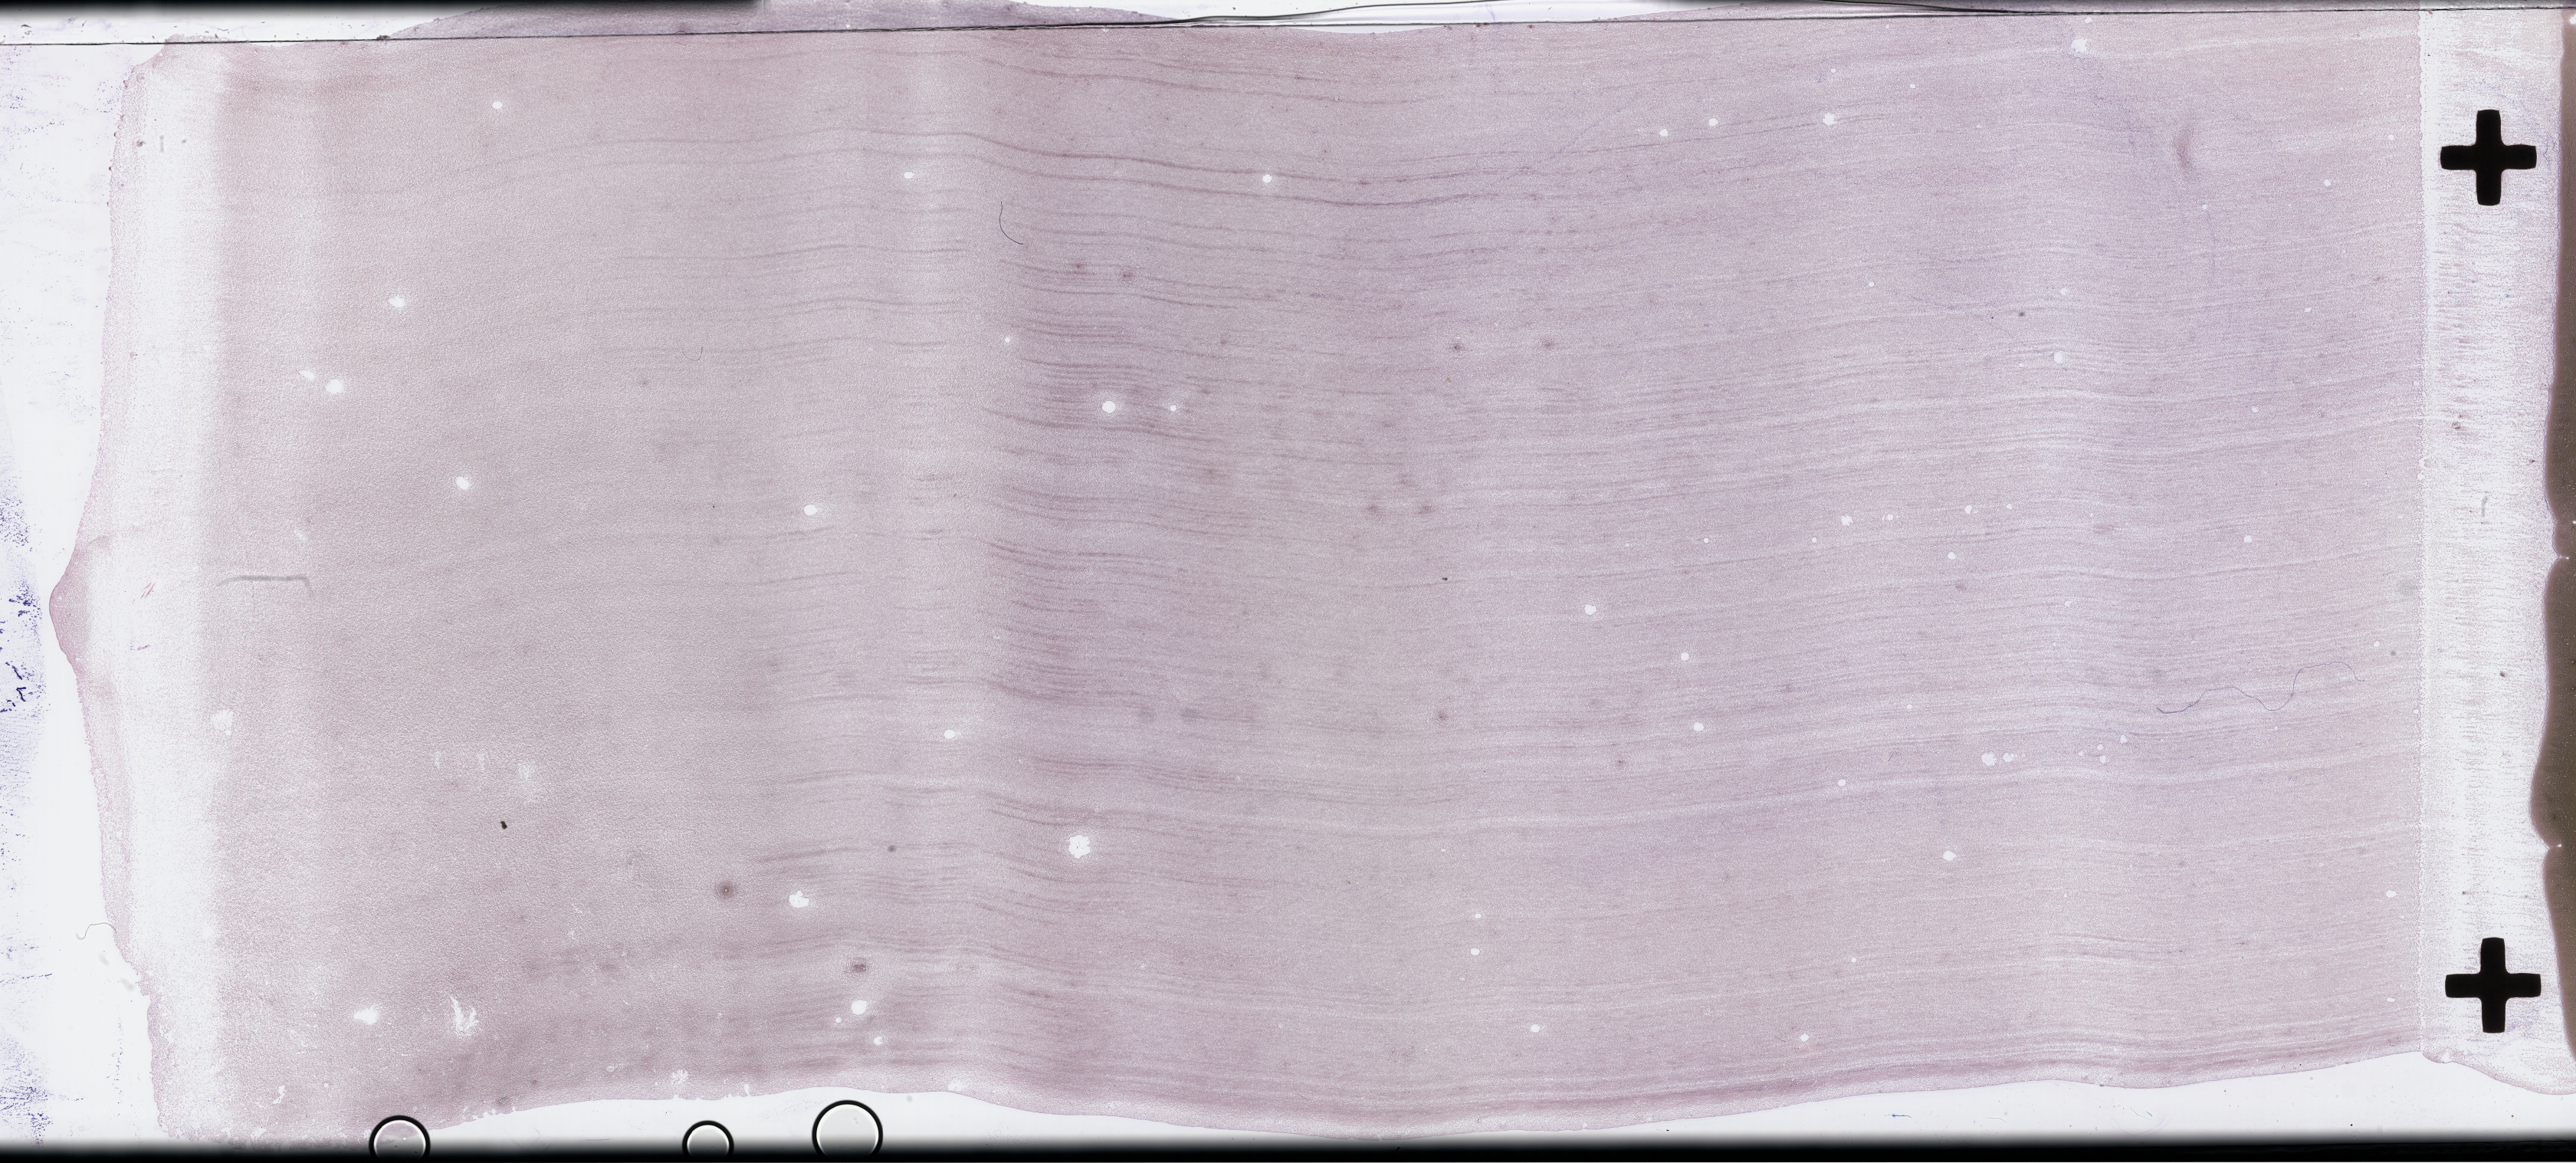
Whole-slide image of a bone marrow smear, Wright-Giemsa stain — a low-resolution overview of the entire scanned area, about 54.3 x 24.5 mm, smear from an EDTA sample, specimen time point: collected at disease progression. Patient sex: male.
Patient diagnosis: Plasma Cell Myeloma.